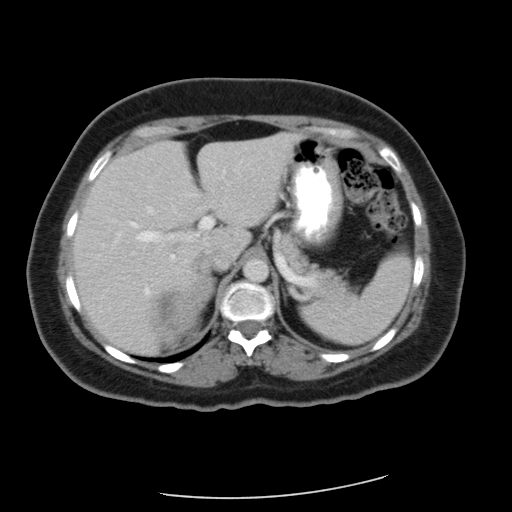
Contrast-enhanced abdominal CT, one axial slice. Slice 41 of 56 in the series (ordered by position). Reconstruction kernel FC12. 120 kVp. Soft-tissue window (W 400 / L 40 HU). 512 × 512 image matrix, field of view 400 × 400 mm. Patient: female, 58 years. Case-level facts recorded for this patient, not image findings: diagnosis: adrenocortical carcinoma; tumour side: right adrenal; tumour size at pathology: 9 cm; Ki-67 index: 25 %; stage (as recorded): 3.
Outlined on this slice (semi-automatic segmentation, software-assisted and operator-edited):
- mass: bounding box [x1, y1, x2, y2] px = [155, 295, 195, 346]